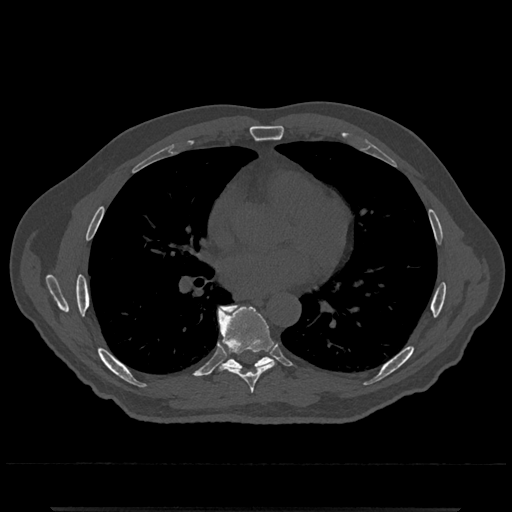
CT including the spine, one axial slice; slice 702 of 797 in the series (ordered by position); bone window (W 1800 / L 400 HU); 0.5 mm slice thickness; 512 × 512 image matrix, field of view 393 × 393 mm. Patient: male, 67 years. From the clinical record (not read from this slice): primary cancer: prostate.
Structures marked on this image (semi-automatic segmentation, software-assisted and operator-edited):
- T7 vertebra: bounding box <218,307,276,394> (left, top, right, bottom; pixels)
- T8 vertebra: <219,304,272,370>